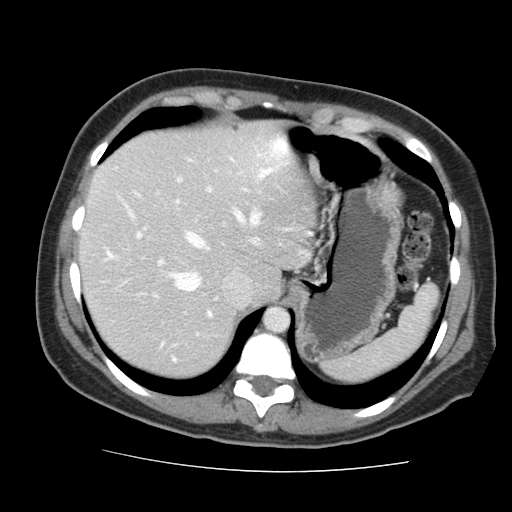
Contrast-enhanced abdominal CT, one axial slice; position 117 of 144 along the scan axis; intravenous contrast given; soft-tissue window (W 400 / L 40 HU); 2.5 mm slice thickness; 512 × 512 image matrix. Female patient, age 46 years. Case-level facts recorded for this patient, not image findings: diagnosis: colorectal cancer liver metastases, imaged before liver resection; multiple liver metastases: no; largest metastasis: 2.8 cm; chemotherapy before resection: yes.
Annotated regions visible in this slice (expert manual segmentation):
- hepatic veins: bounding box [x1, y1, x2, y2] px = [108, 169, 272, 291]
- liver: [82, 126, 313, 376]
- planned liver remnant (the part of the liver to remain after resection): [82, 126, 313, 376]
- portal vein (with intrahepatic branches): [107, 179, 247, 361]